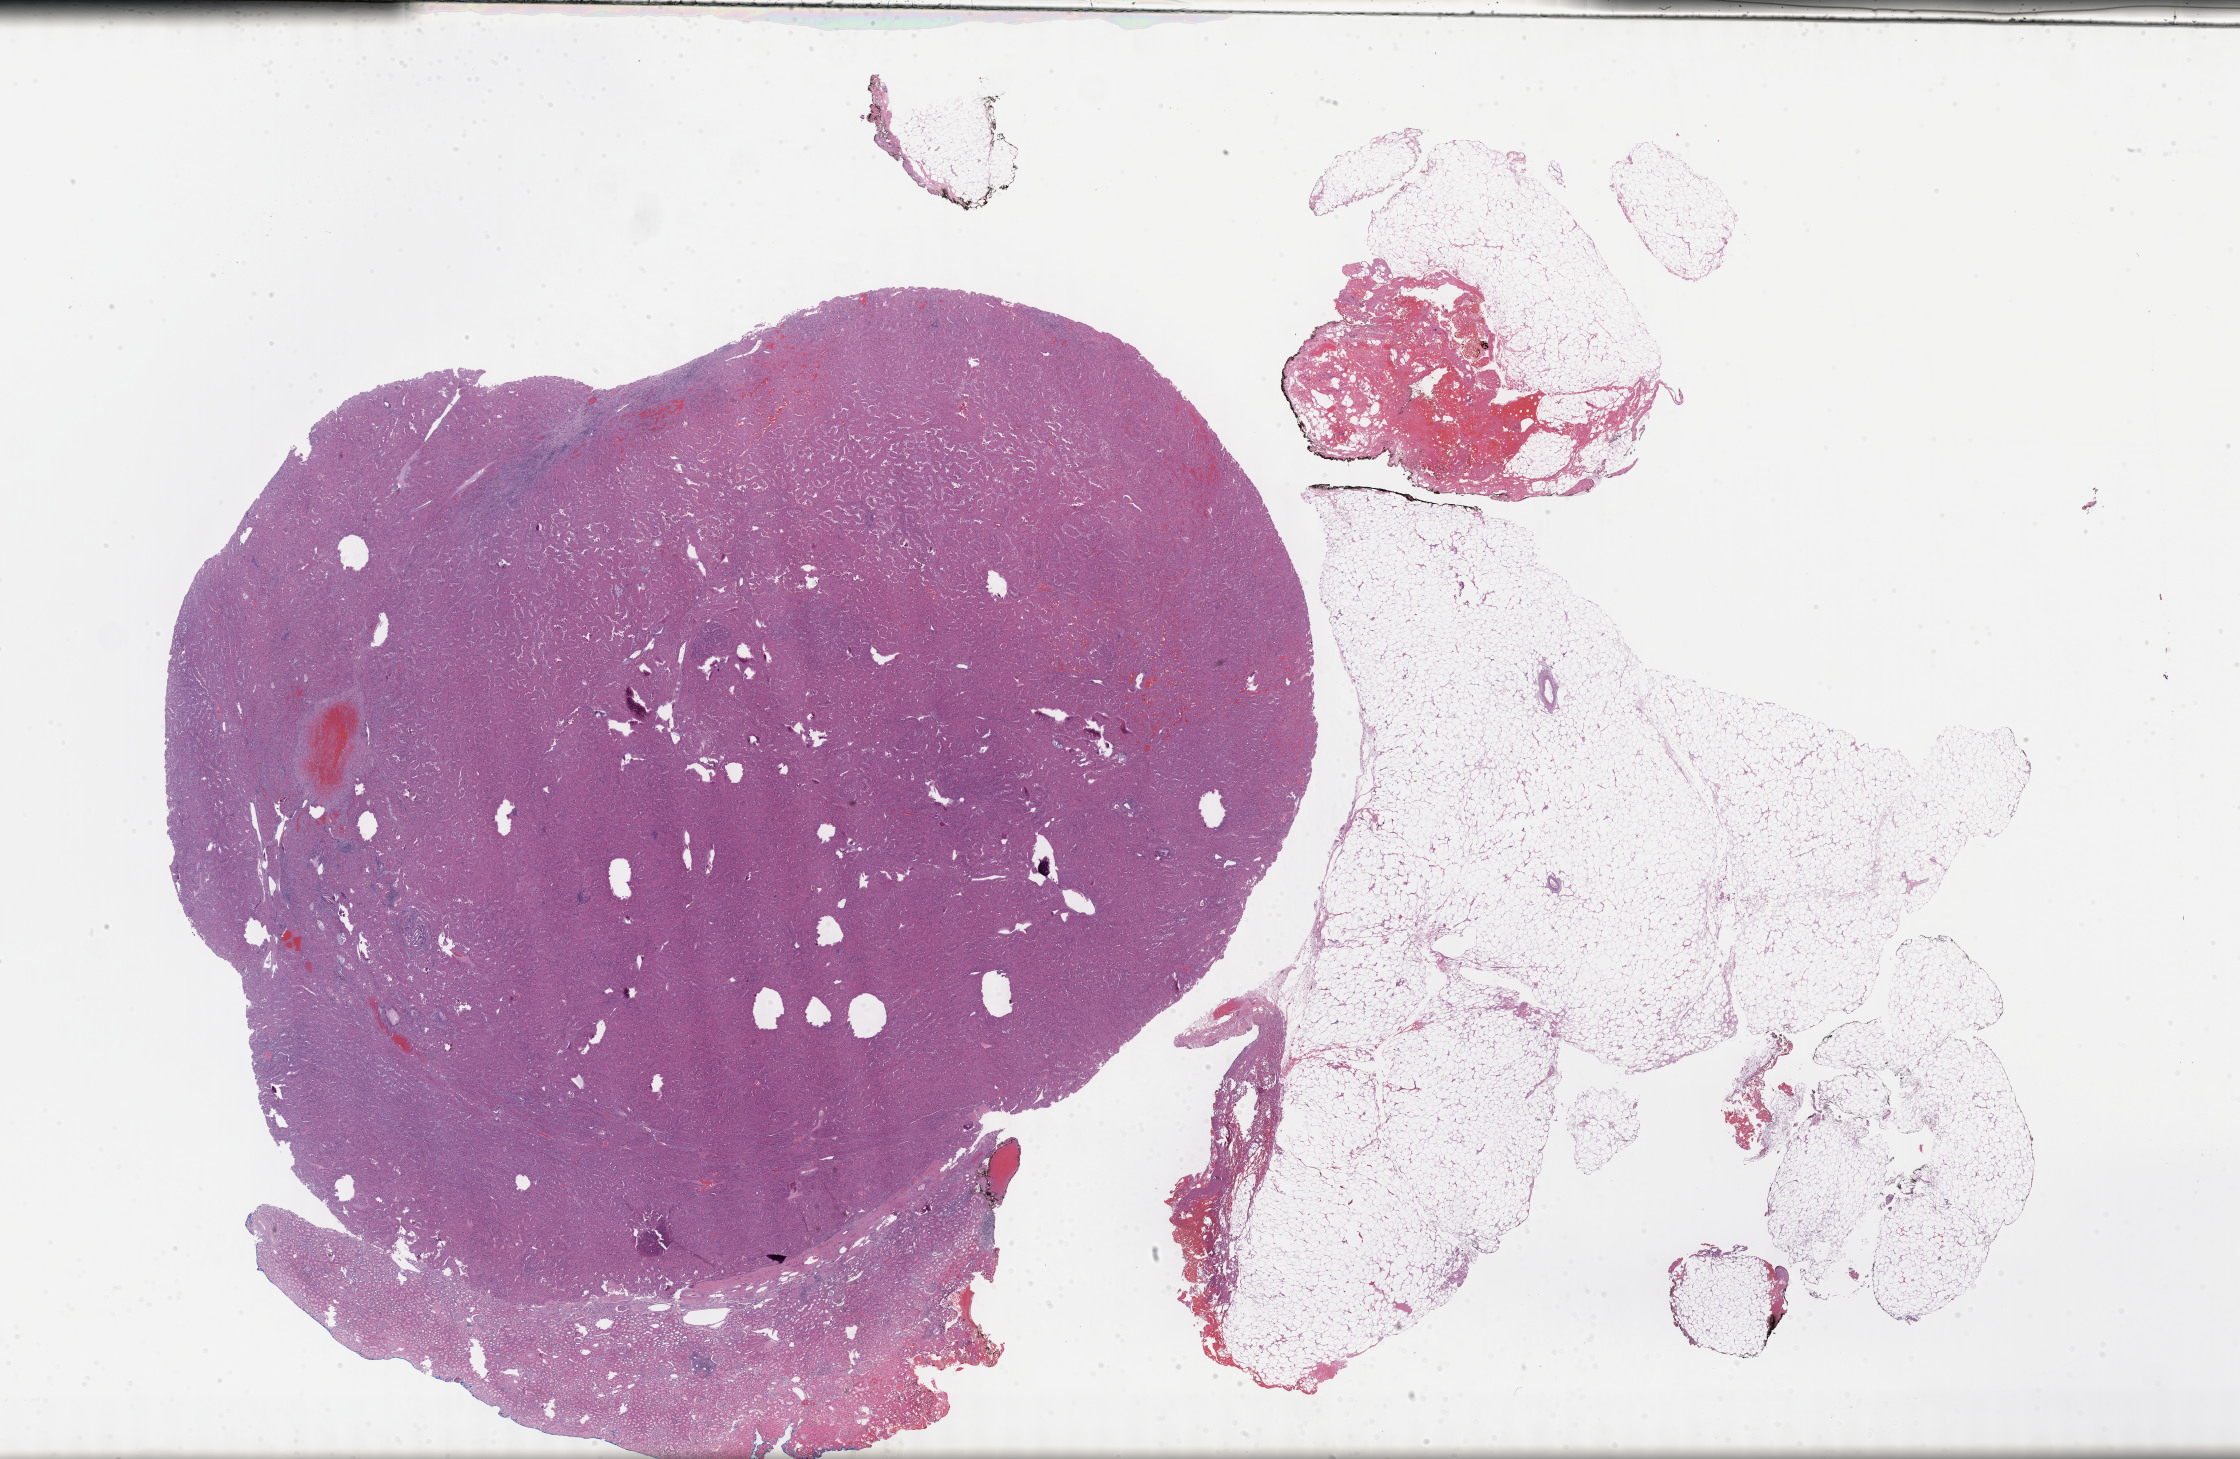
Hematoxylin and eosin (H&E) stained whole-slide image, whole scanned area (about 36.2 x 23.6 mm, acquisition: 40x scan) shown as a low-resolution overview; formalin-fixed paraffin-embedded (FFPE) diagnostic section; sample: primary tumour, kidney. Patient: male, age at initial diagnosis 62 years.
* TNM: T1a NX MX
* AJCC pathologic stage: I (7th edition)
* diagnosis: Papillary adenocarcinoma, NOS